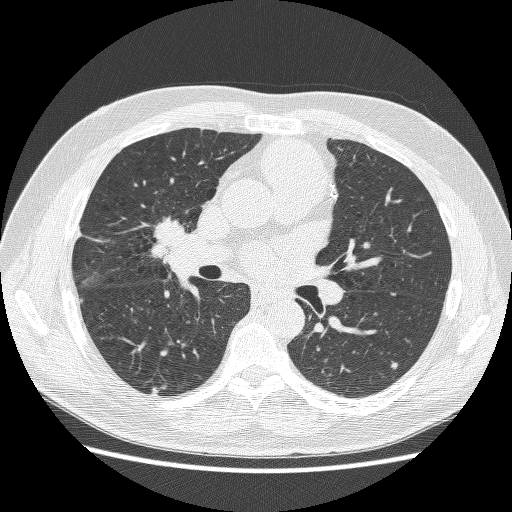
Axial slice from a low-dose chest CT screening exam; baseline annual screen; lung window (W 1500 / L -600 HU); 1.25 mm slice thickness; lung (sharp) reconstruction kernel (BONE). Male, age 59 years at enrolment. Former smoker at enrolment.
• Expert reader's lesion annotation, bounding box [x1, y1, x2, y2] px = [130, 213, 198, 275].
• Screening reader's record for this exam: no non-calcified nodule ≥4 mm recorded.
• Later outcome: lung cancer diagnosed 24 days after this screen — adenocarcinoma, NOS, right middle lobe, poorly differentiated (G3), stage IV (AJCC 6th edition), 54 mm at pathology.